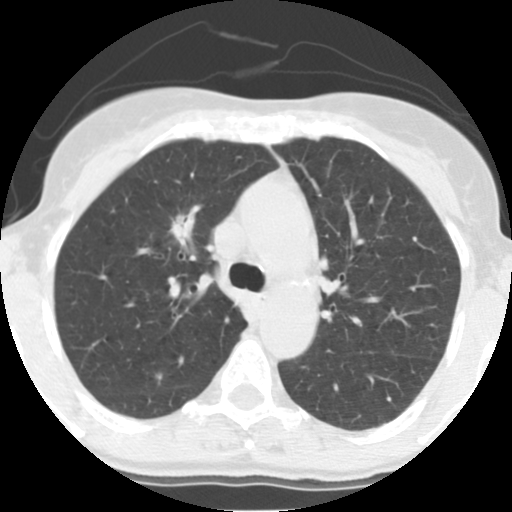
Axial slice from a low-dose chest CT screening exam; third screening round (two years after baseline); lung window (W 1500 / L -600 HU); 2.5 mm slice thickness. Female, age 56 years at enrolment. Former smoker at enrolment.
• Lesion marked by an expert reader, bounding box (x1, y1, x2, y2) in pixels: (161, 210, 198, 246).
• The exam's reader record, not a measurement of the box and not confirmed to be the same lesion: non-calcified nodule or mass ≥4 mm, right upper lobe, 17 × 12 mm, spiculated (stellate) margins, soft tissue attenuation, pre-existing on the prior screen: yes; interval growth: yes.
• Official screen result: positive, other.
• Later outcome: lung cancer diagnosed 49 days after this screen — adenocarcinoma, NOS, right upper lobe, moderately differentiated (G2), stage IA (AJCC 6th edition), 19 mm at pathology.